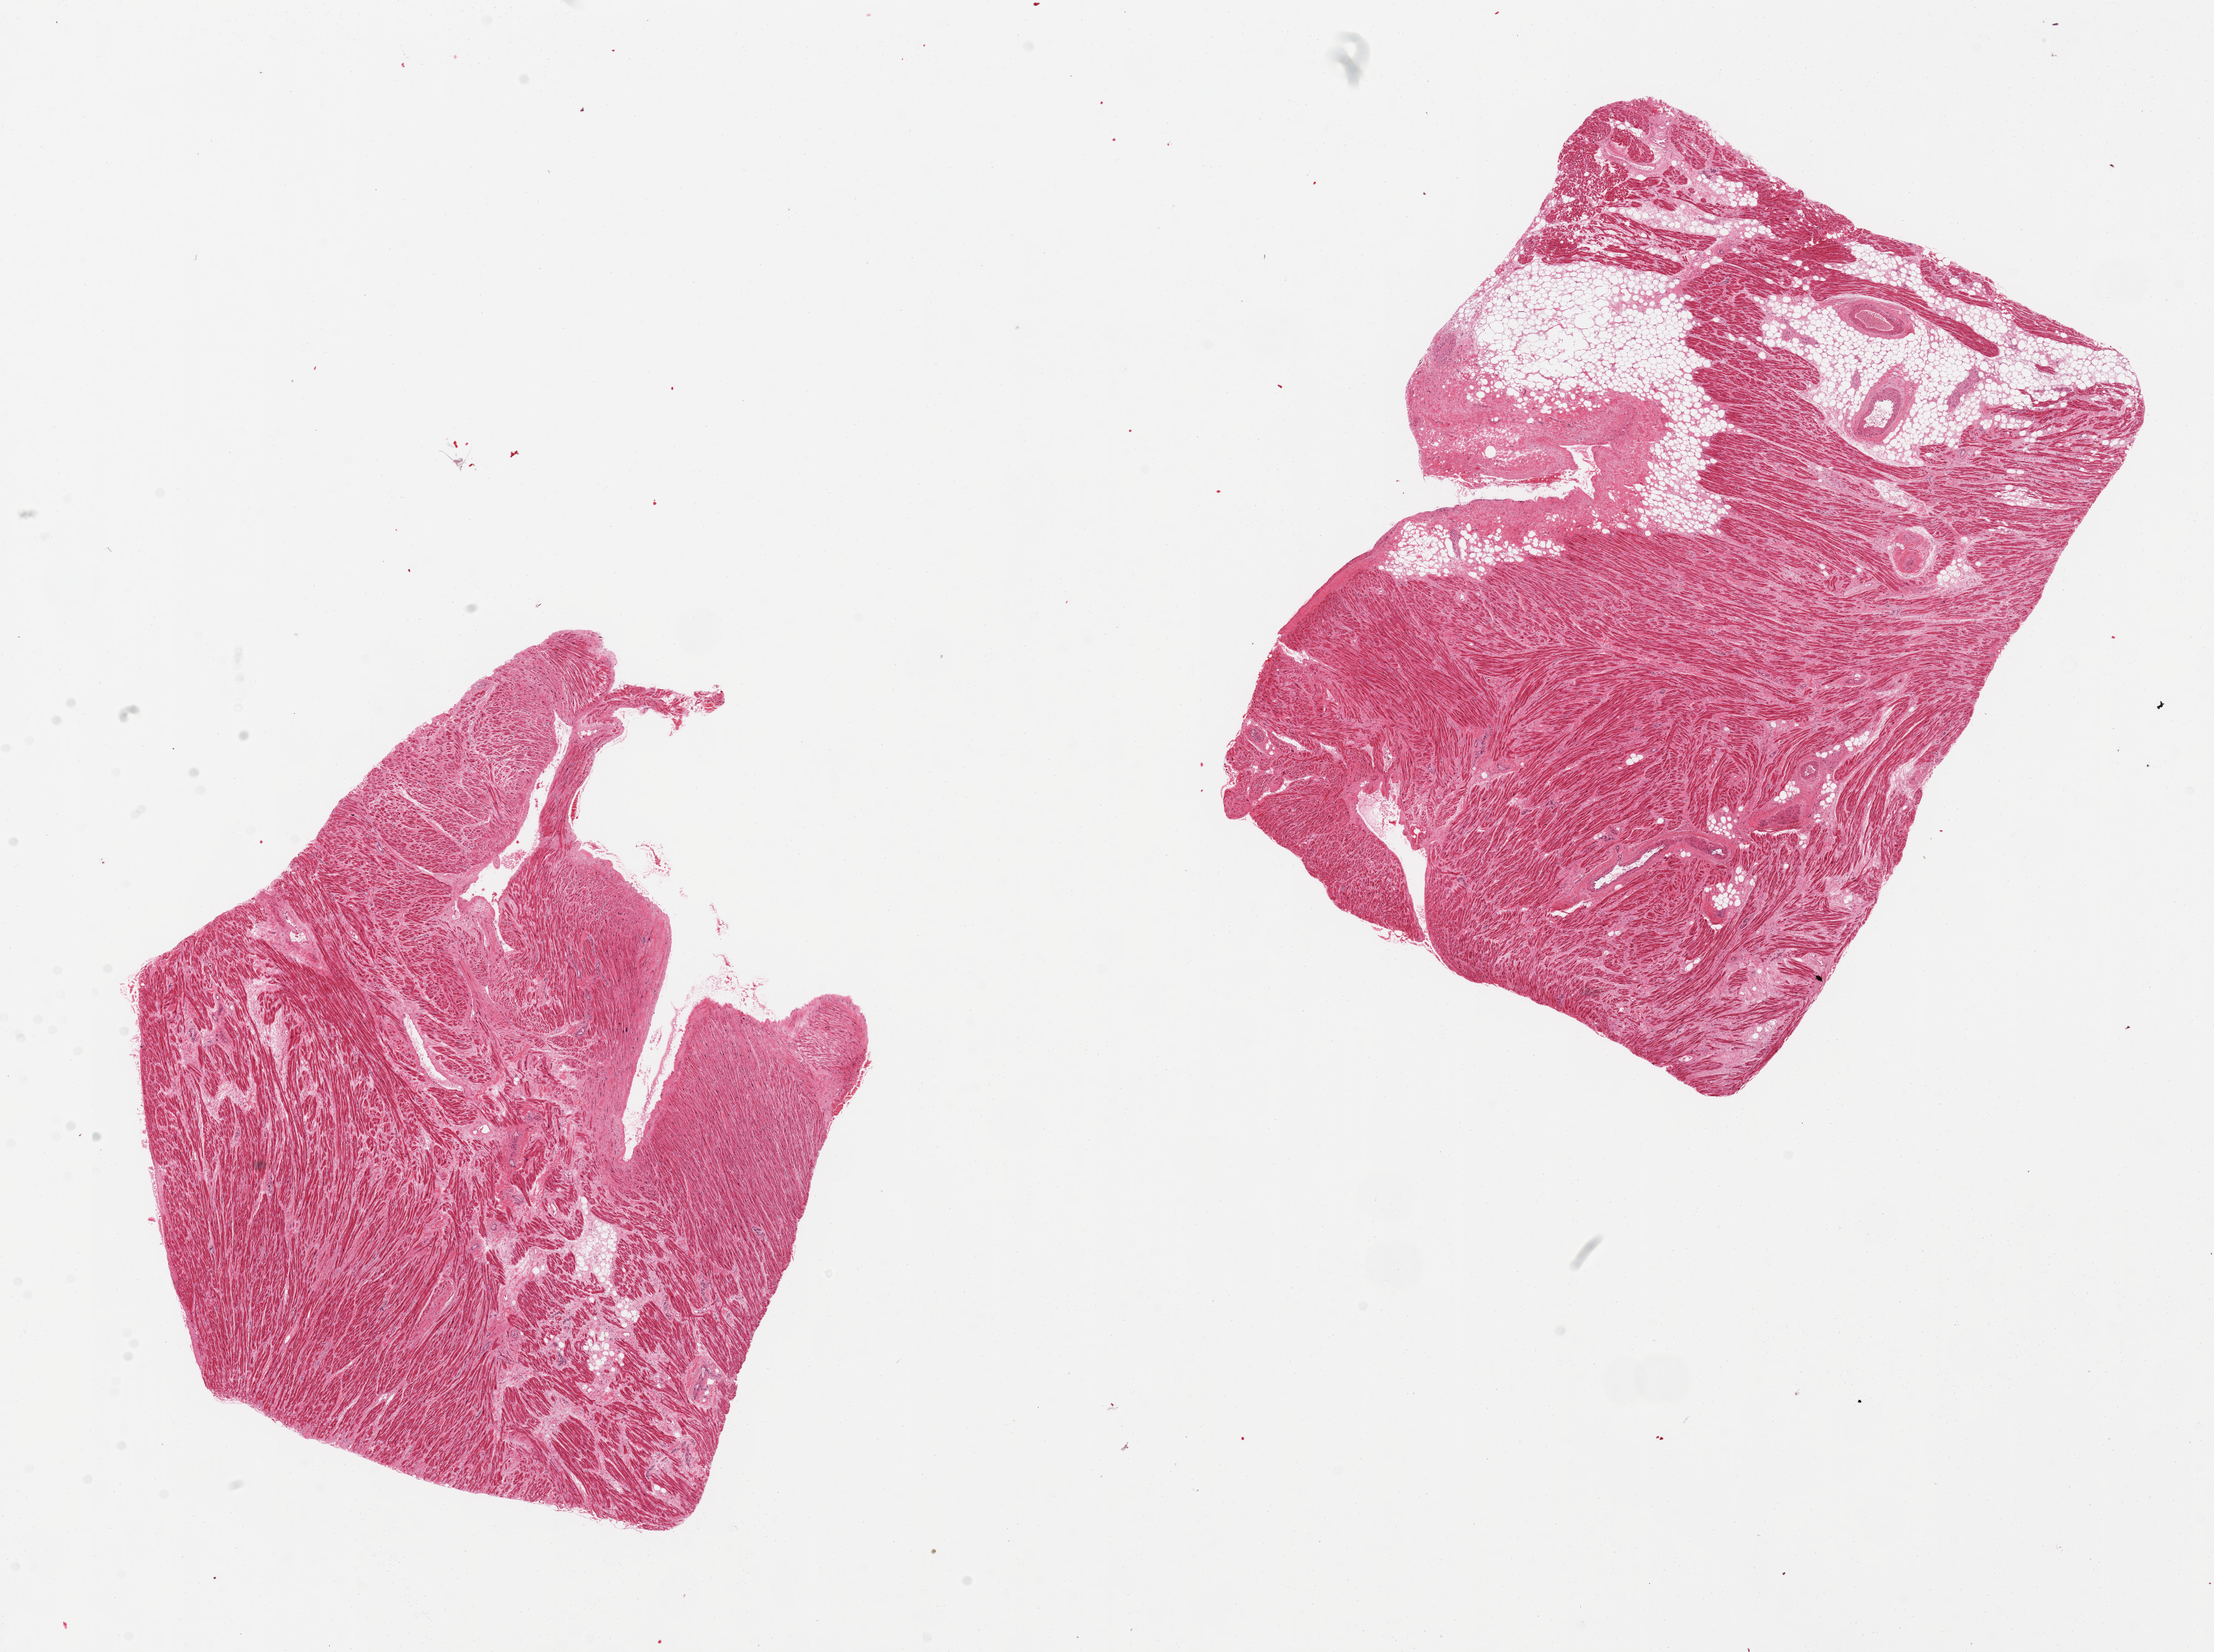
Whole-slide image, haematoxylin and eosin stain, brightfield, low-resolution overview of the scanned area, about 23.6 x 17.6 mm; PAXgene-fixed paraffin-embedded (PFPE) section; section of auricular appendage (target tissue); tissue donor sample. Male donor.
* pathologist's review note for this sample: 2 pieces; 1 has 20% fat